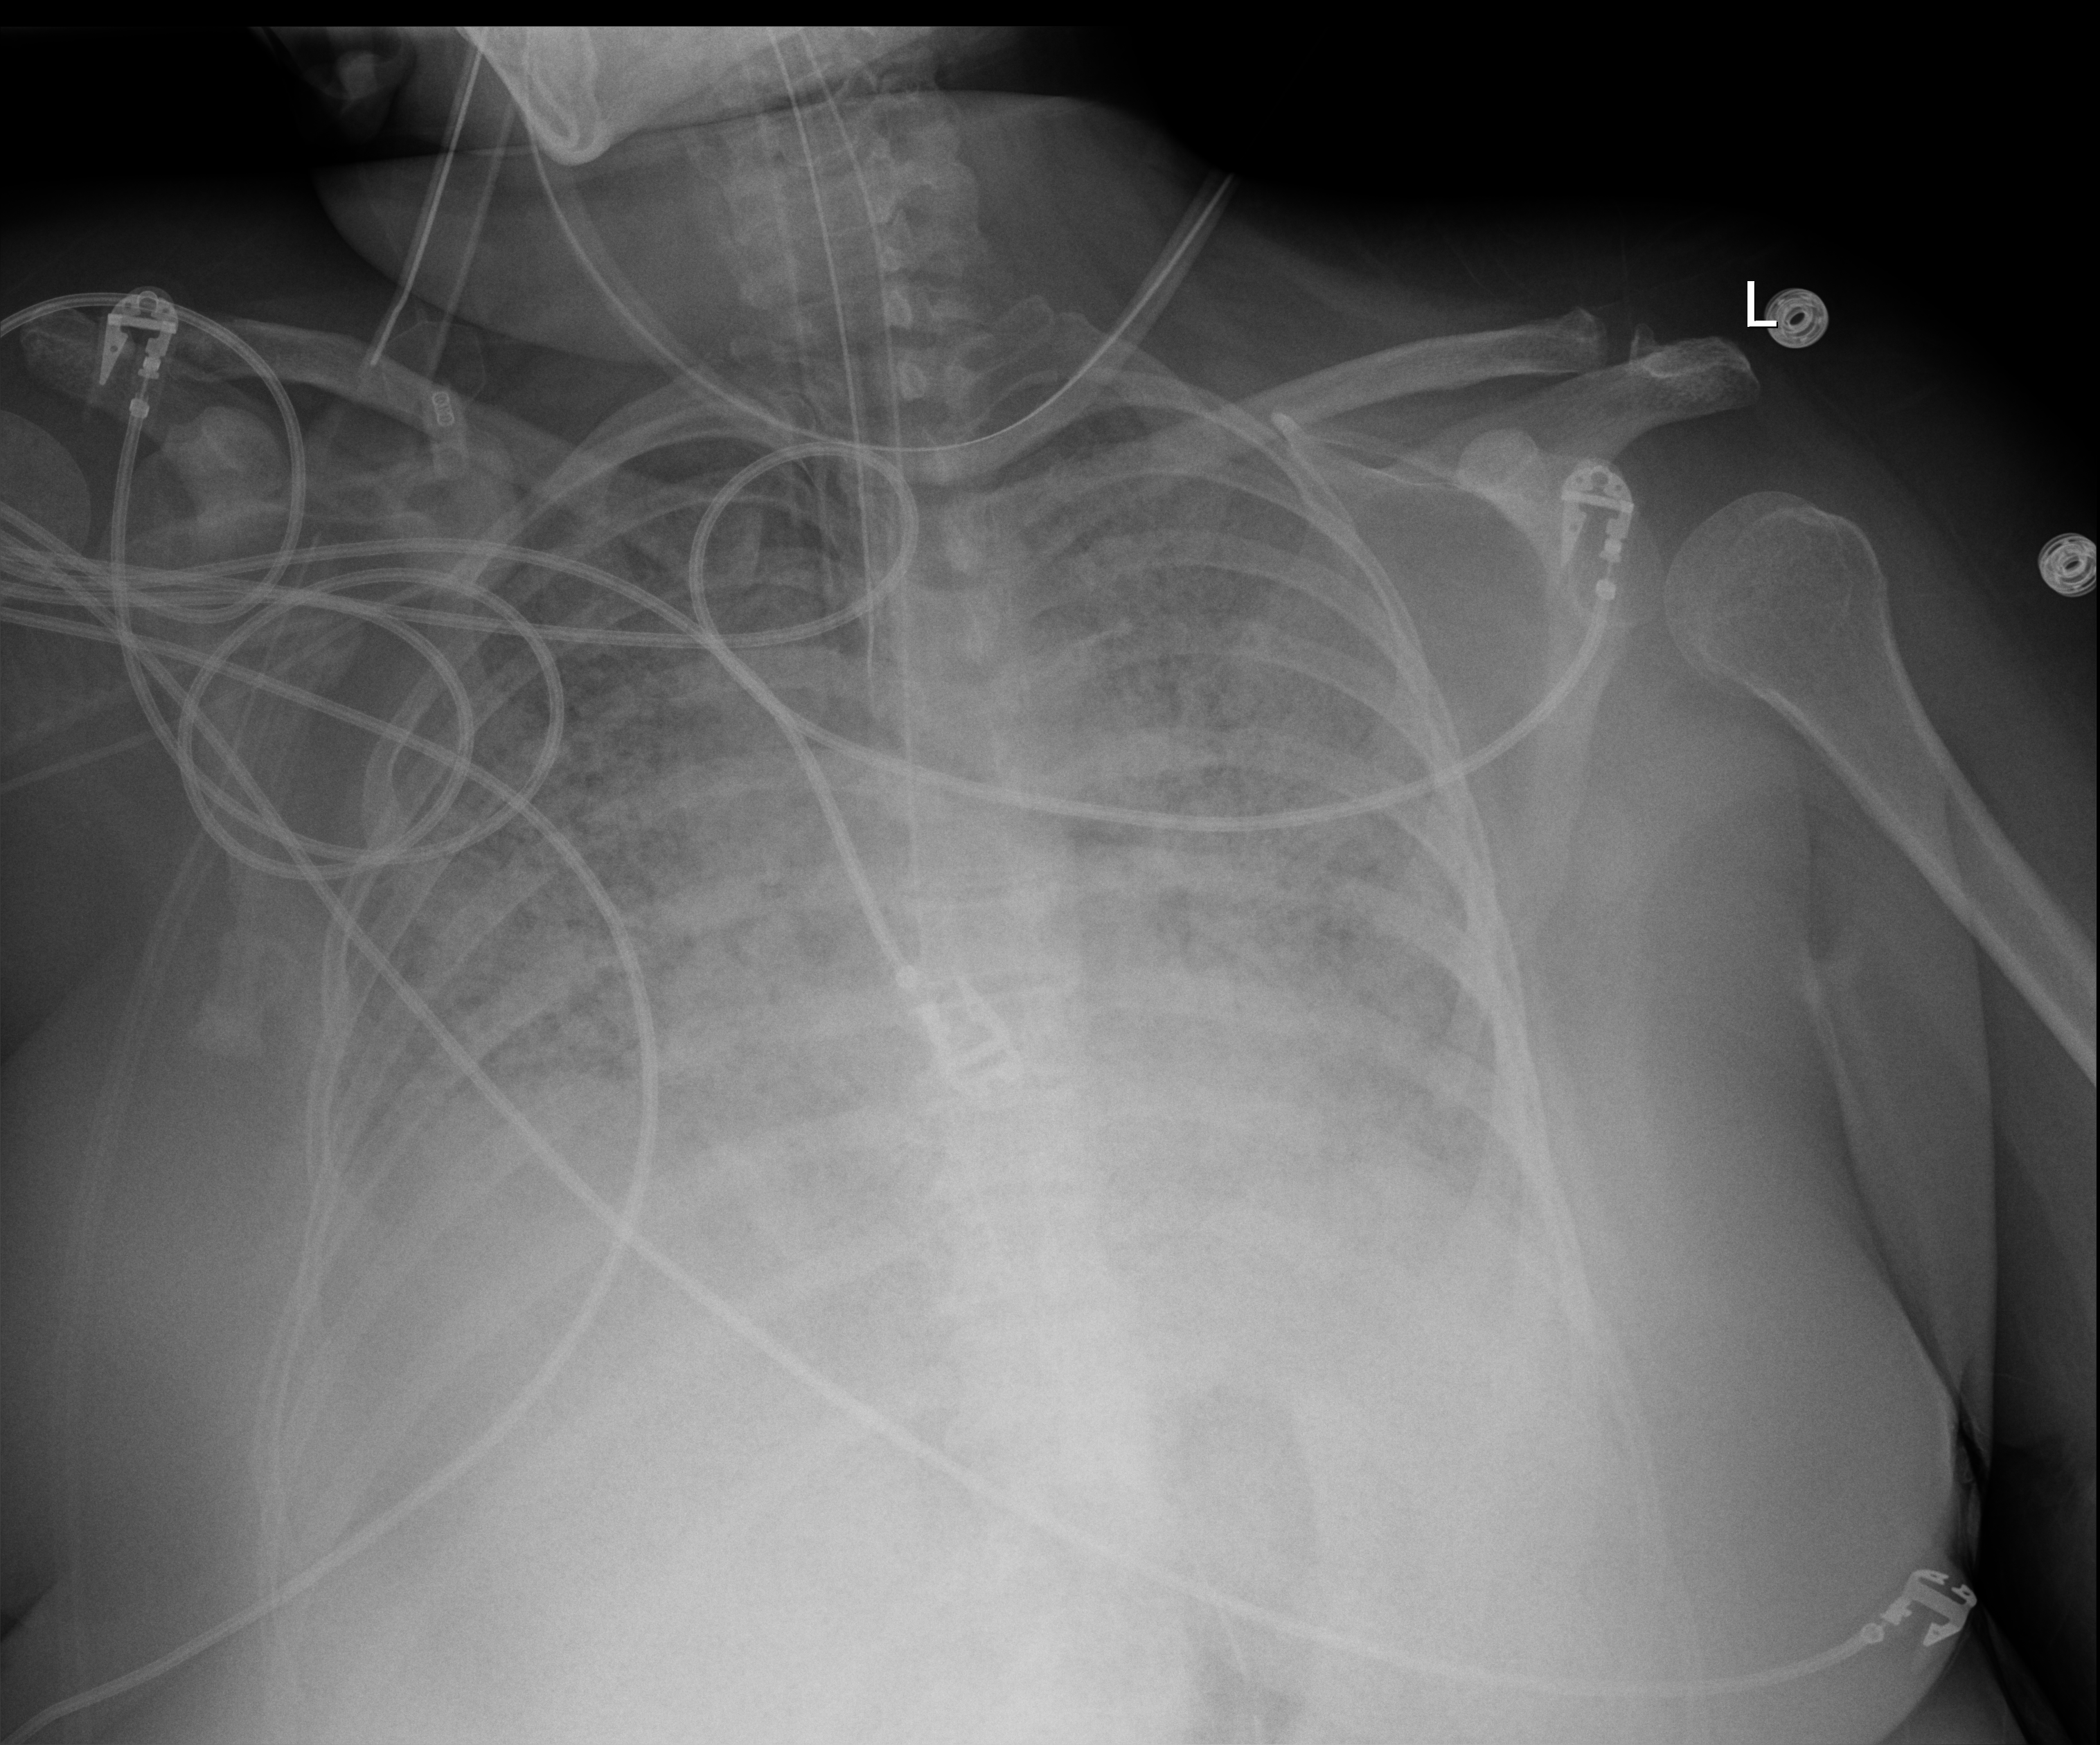
Chest X-ray (portable), anteroposterior (AP) projection. Female patient hospitalised with COVID-19, age 18–59 years.
From the hospital-stay record, not from the radiograph (when in the stay this image was taken is not recorded): COPD (admission record): no.